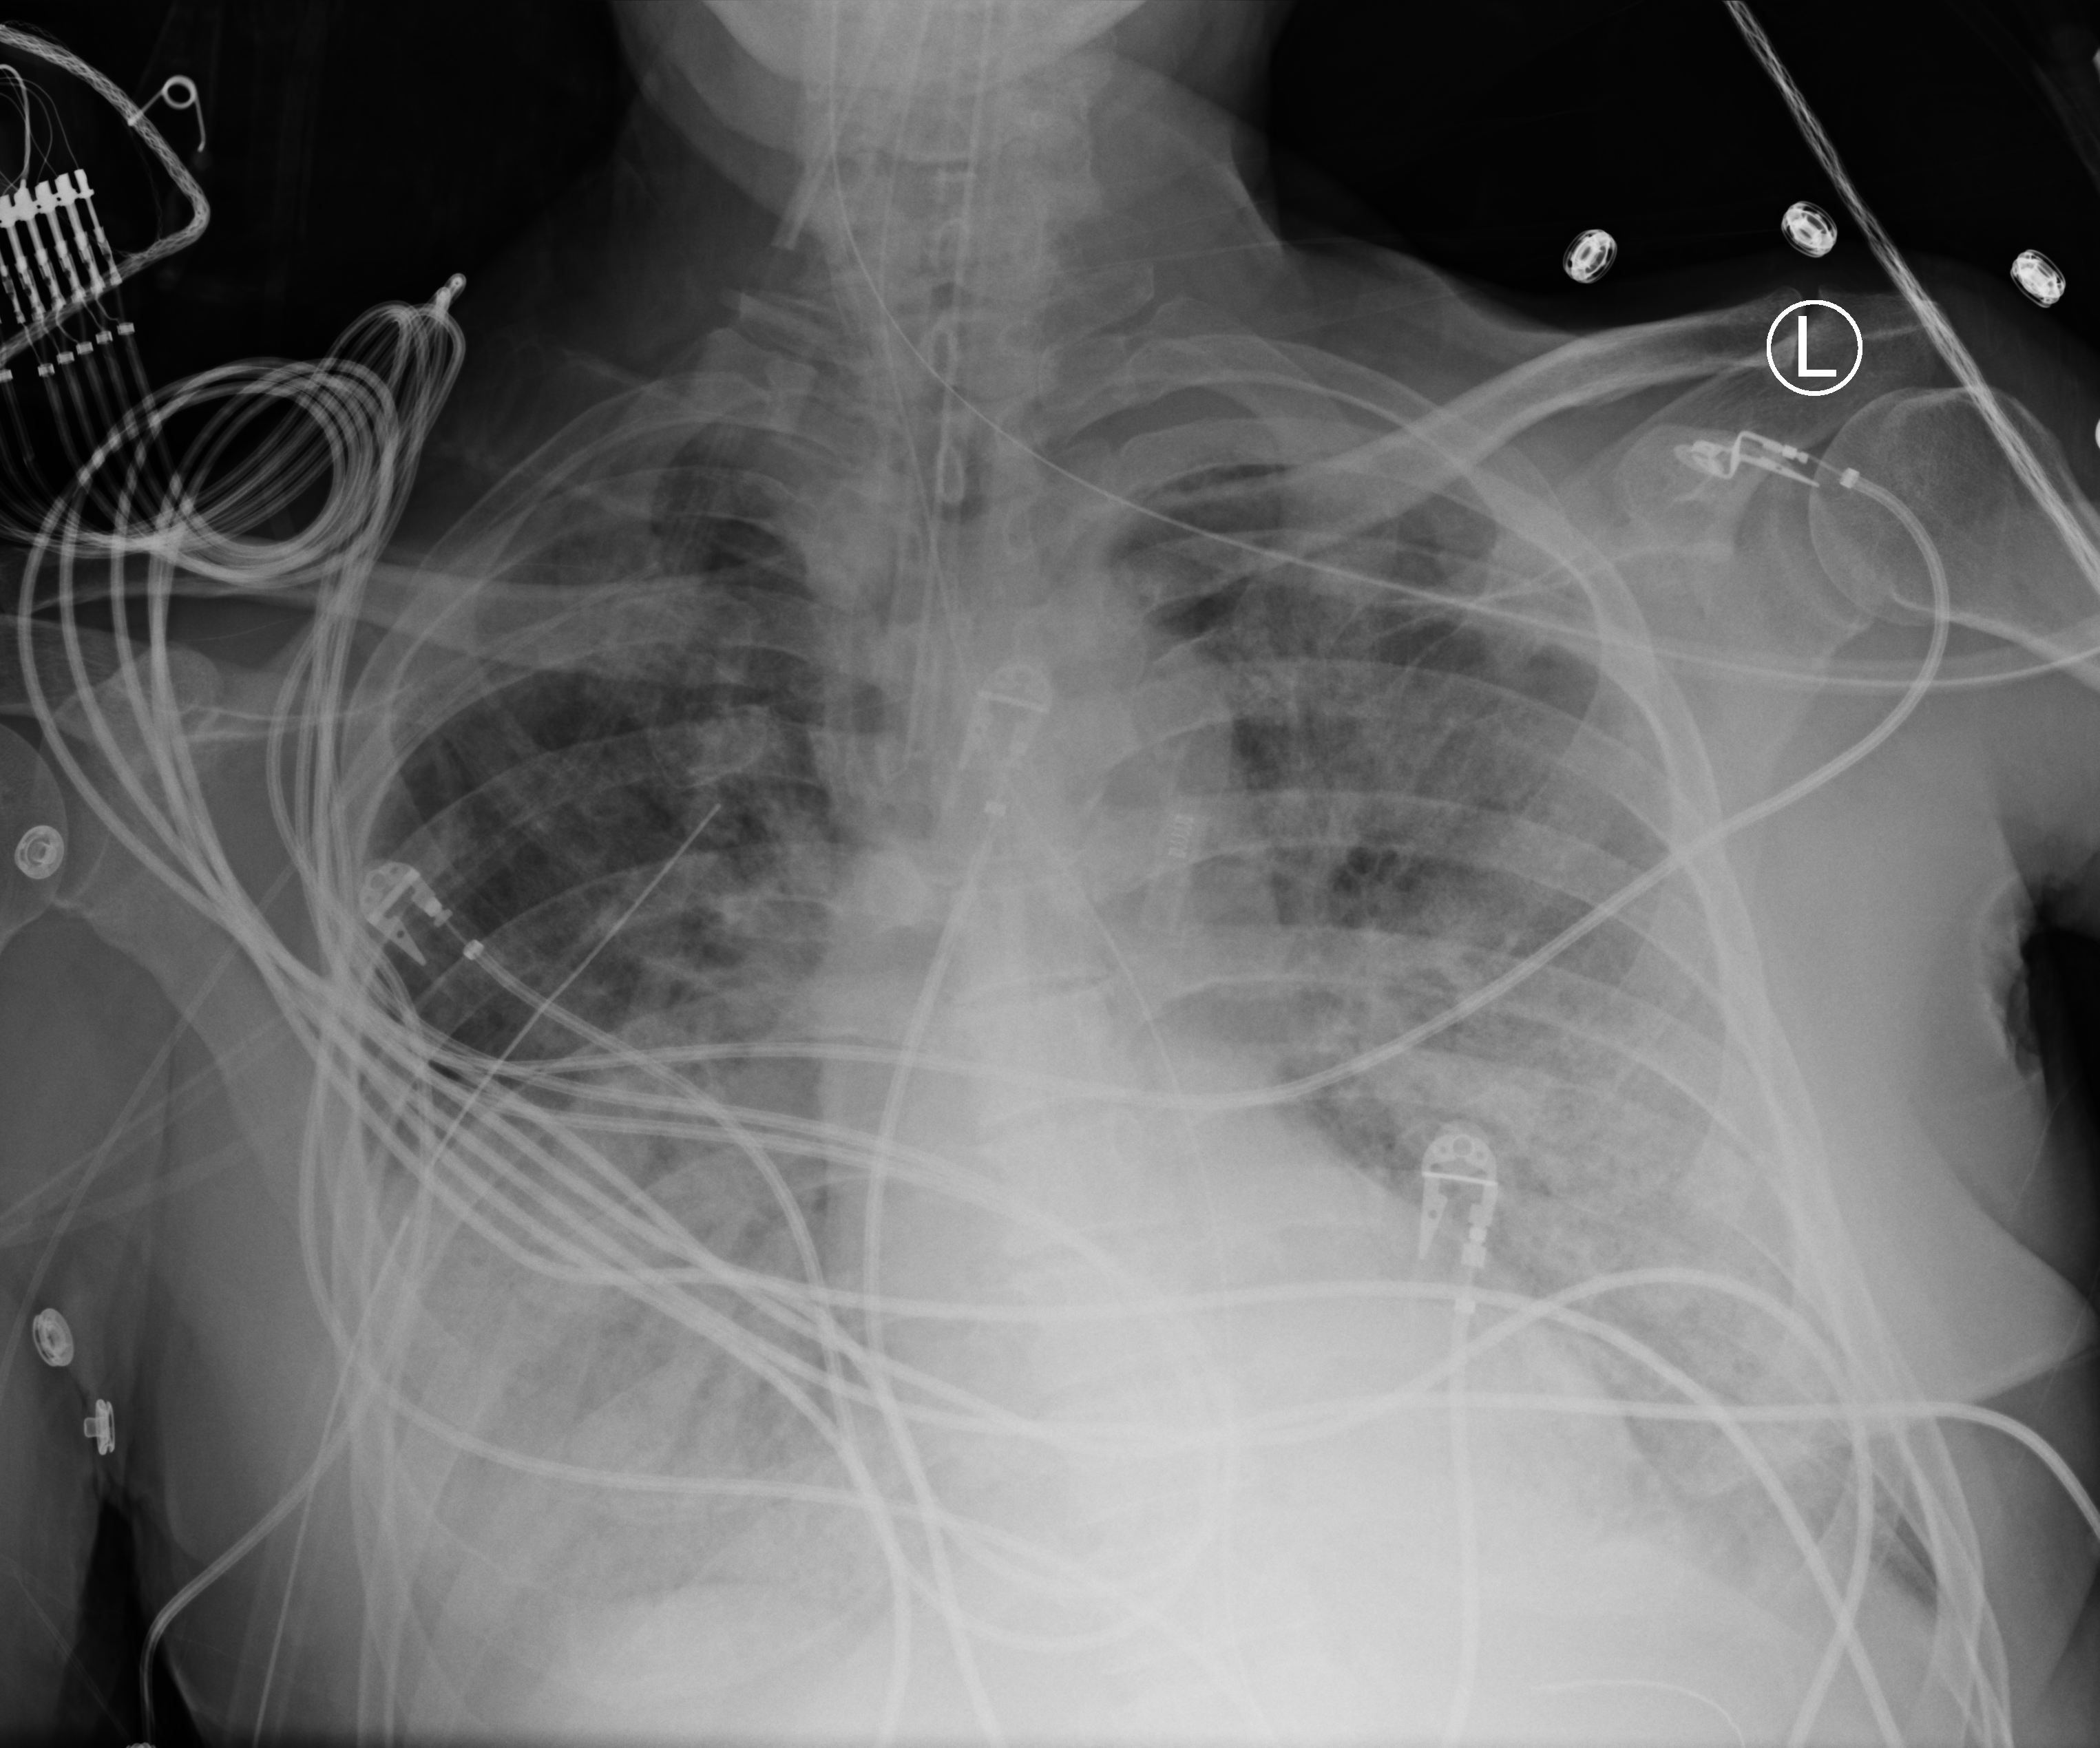
Portable chest radiograph, anteroposterior (AP) projection. Patient hospitalised with COVID-19; male, aged 60–74 years.
Hospital-stay facts (about this admission, not read from this image; timing relative to this image not recorded):
- mechanically ventilated during this hospital stay: yes
- admitted to intensive care during this hospital stay: yes
- hypertension (admission record): no